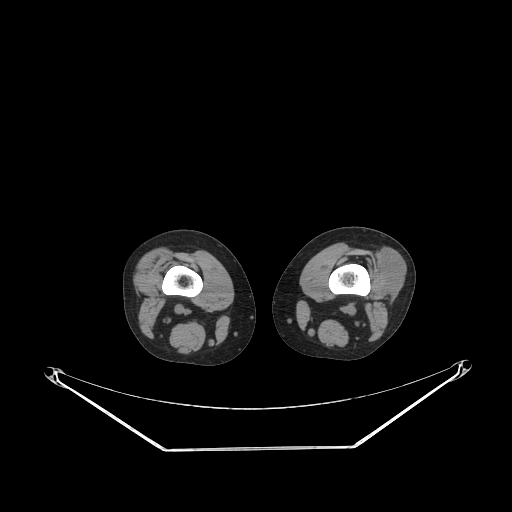
CT of an extremity soft-tissue mass (from a PET/CT study), one axial slice; slice 176 of 223 in the series (ordered by position); reconstruction kernel STANDARD; 140 kVp; soft-tissue window (W 400 / L 40 HU); 512 × 512 image matrix, field of view 500 × 500 mm. Female patient. From the clinical record (not read from this slice): histological type: spindle cell suggestive of biphasic synovial sarcoma; grade: intermediate; site of the primary tumour: left knee.
Outlined on this slice (expert contour drawn on MRI and transferred to this co-registered scan by the dataset authors):
- gross tumour volume including surrounding oedema: bounding box [x1, y1, x2, y2] px = [374, 244, 405, 295]
- gross tumour volume (mass): [377, 246, 405, 295]